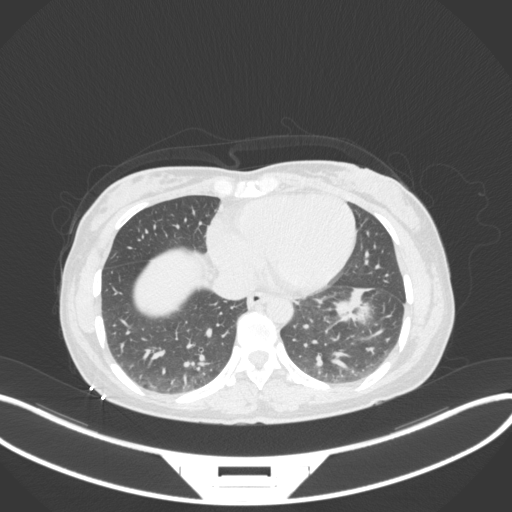
Chest CT, one axial slice. Position 119 of 361 along the scan axis. Reconstruction kernel B31f. 120 kVp. Lung window (W 1500 / L -600 HU). 1 mm slice thickness. 512 × 512 image matrix, field of view 400 × 400 mm. Female patient, age 41 years. From the clinical record (not read from this slice): clinical TNM (as recorded): T2a N3 M1b.
Outlined on this slice (rectangle marked by the reading radiologist):
- lung tumour (recorded histology: adenocarcinoma): bounding box (x1, y1, x2, y2) in pixels: (328, 283, 374, 327)